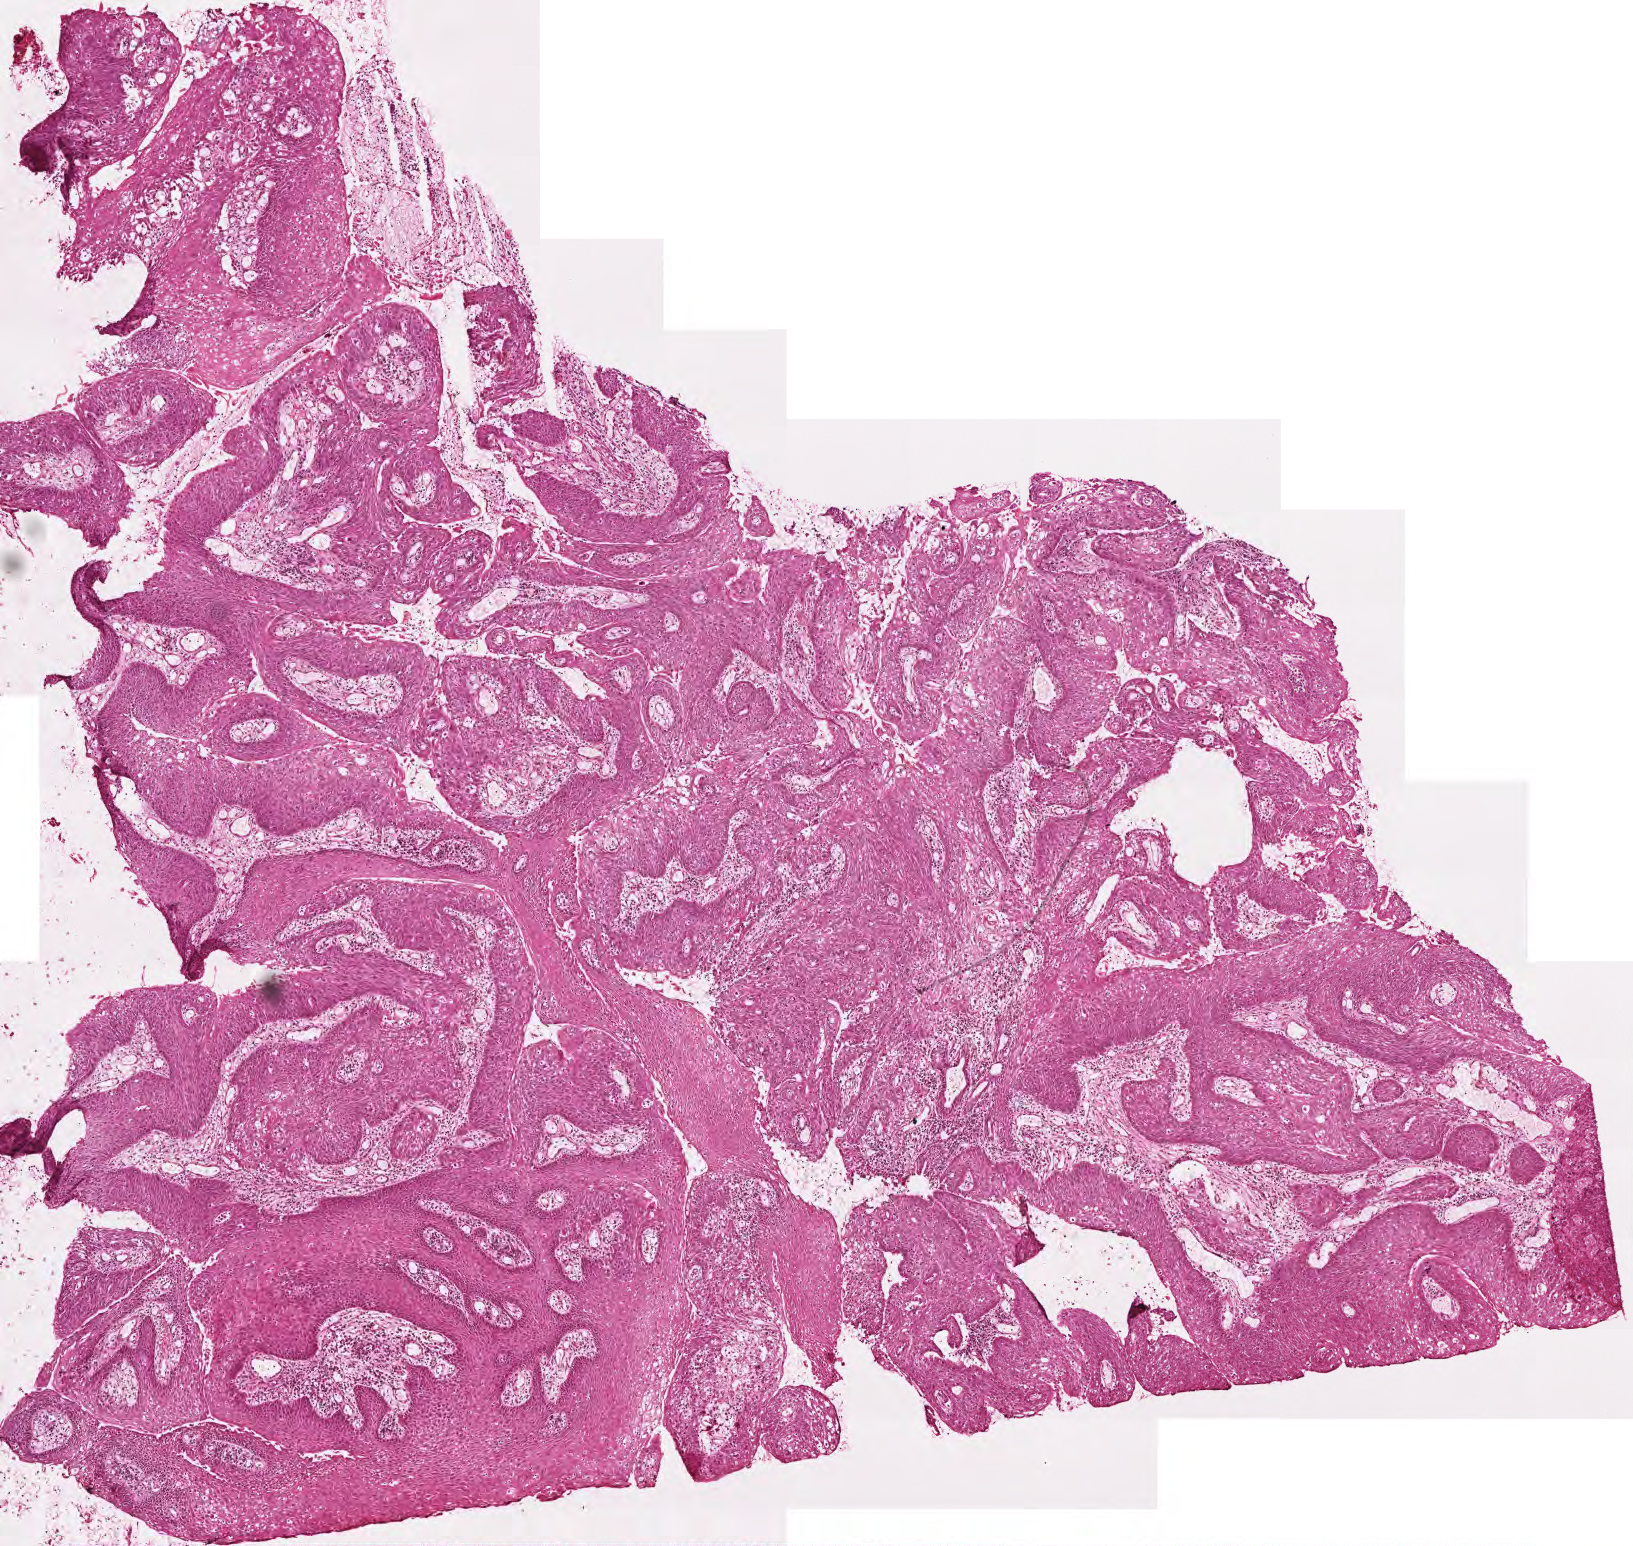
Digitized Hematoxylin and eosin (H&E) stained tissue section (whole slide), low-resolution overview of the scanned area, about 3.3 x 3.1 mm. Frozen section from the top of the tissue portion. Head and neck, primary tumour sample. Patient: male, age at initial diagnosis 66 years. Histologic grade: G2 (moderately differentiated). Slide review estimates, as recorded: tumour cells 88%, tumour nuclei 75%, normal cells 0%, stromal cells 12%, necrosis 0%.
* diagnosis: Squamous cell carcinoma, NOS (larynx, NOS)
* AJCC pathologic stage: III